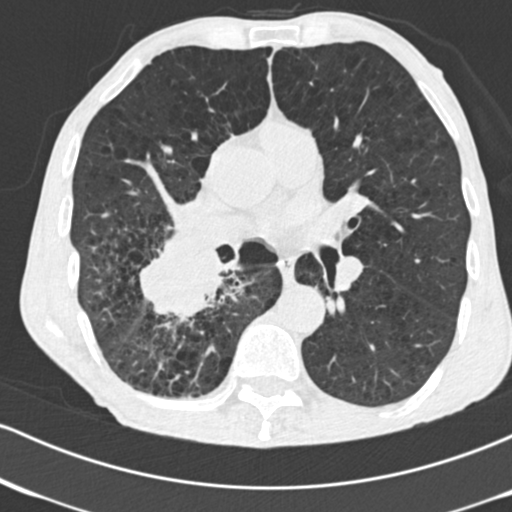
Axial slice from a low-dose chest CT screening exam; second screening round (one year after baseline); lung window (W 1500 / L -600 HU); 2 mm slice thickness; 120 kVp; 512 × 512 image matrix, field of view 316 × 316 mm. Male participant, aged 64 years at enrolment. Current smoker at enrolment.
Expert reader's lesion annotation, bounding box <129,229,239,332> (left, top, right, bottom; pixels). Screening reader's record for this exam (one nodule recorded; not confirmed to be the boxed lesion): non-calcified nodule or mass ≥4 mm, 52 × 37 mm, spiculated (stellate) margins, soft tissue attenuation, pre-existing on the prior screen: no. Participant outcome: lung cancer diagnosed 28 days after this screen — adenocarcinoma, NOS, right lower lobe, stage IV (AJCC 6th edition), 60 mm at pathology.